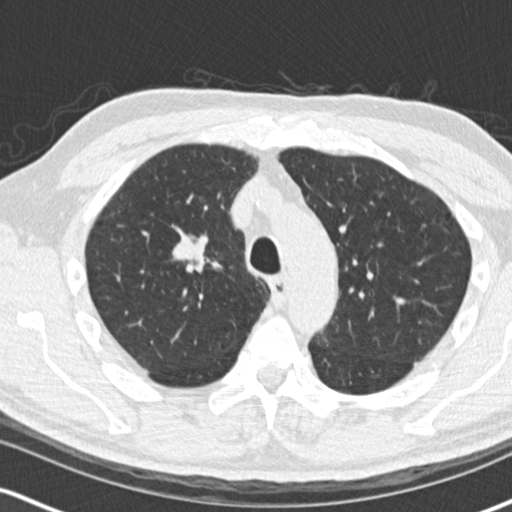
Low-dose screening chest CT, one axial slice. Position 113 of 170 along the scan axis. Reconstruction kernel B30f. Lung window (W 1500 / L -600 HU). 2 mm slice thickness. 512 × 512 image matrix, field of view 320 × 320 mm.
Annotated regions visible in this slice (outlined manually by an expert reader):
- lesion 1 (tumor, upper lobe of right lung): box from (x=172, y=239) to (x=205, y=262) px